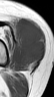
MRI of an extremity soft-tissue mass, one axial slice. Slice 26 of 42 in the series (ordered by position). MR volume resampled by the dataset authors to the PET/CT grid (not the native acquisition matrix). 54 × 97 image matrix. Female patient. From the clinical record (not read from this slice): histological type: spindle cell suggestive of biphasic synovial sarcoma; grade: intermediate; site of the primary tumour: left knee.
Outlined on this slice (expert contour drawn on MRI and transferred to this co-registered scan by the dataset authors):
- gross tumour volume including surrounding oedema: bounding box <17,18,45,67> (left, top, right, bottom; pixels)
- gross tumour volume (mass): <17,19,45,67>